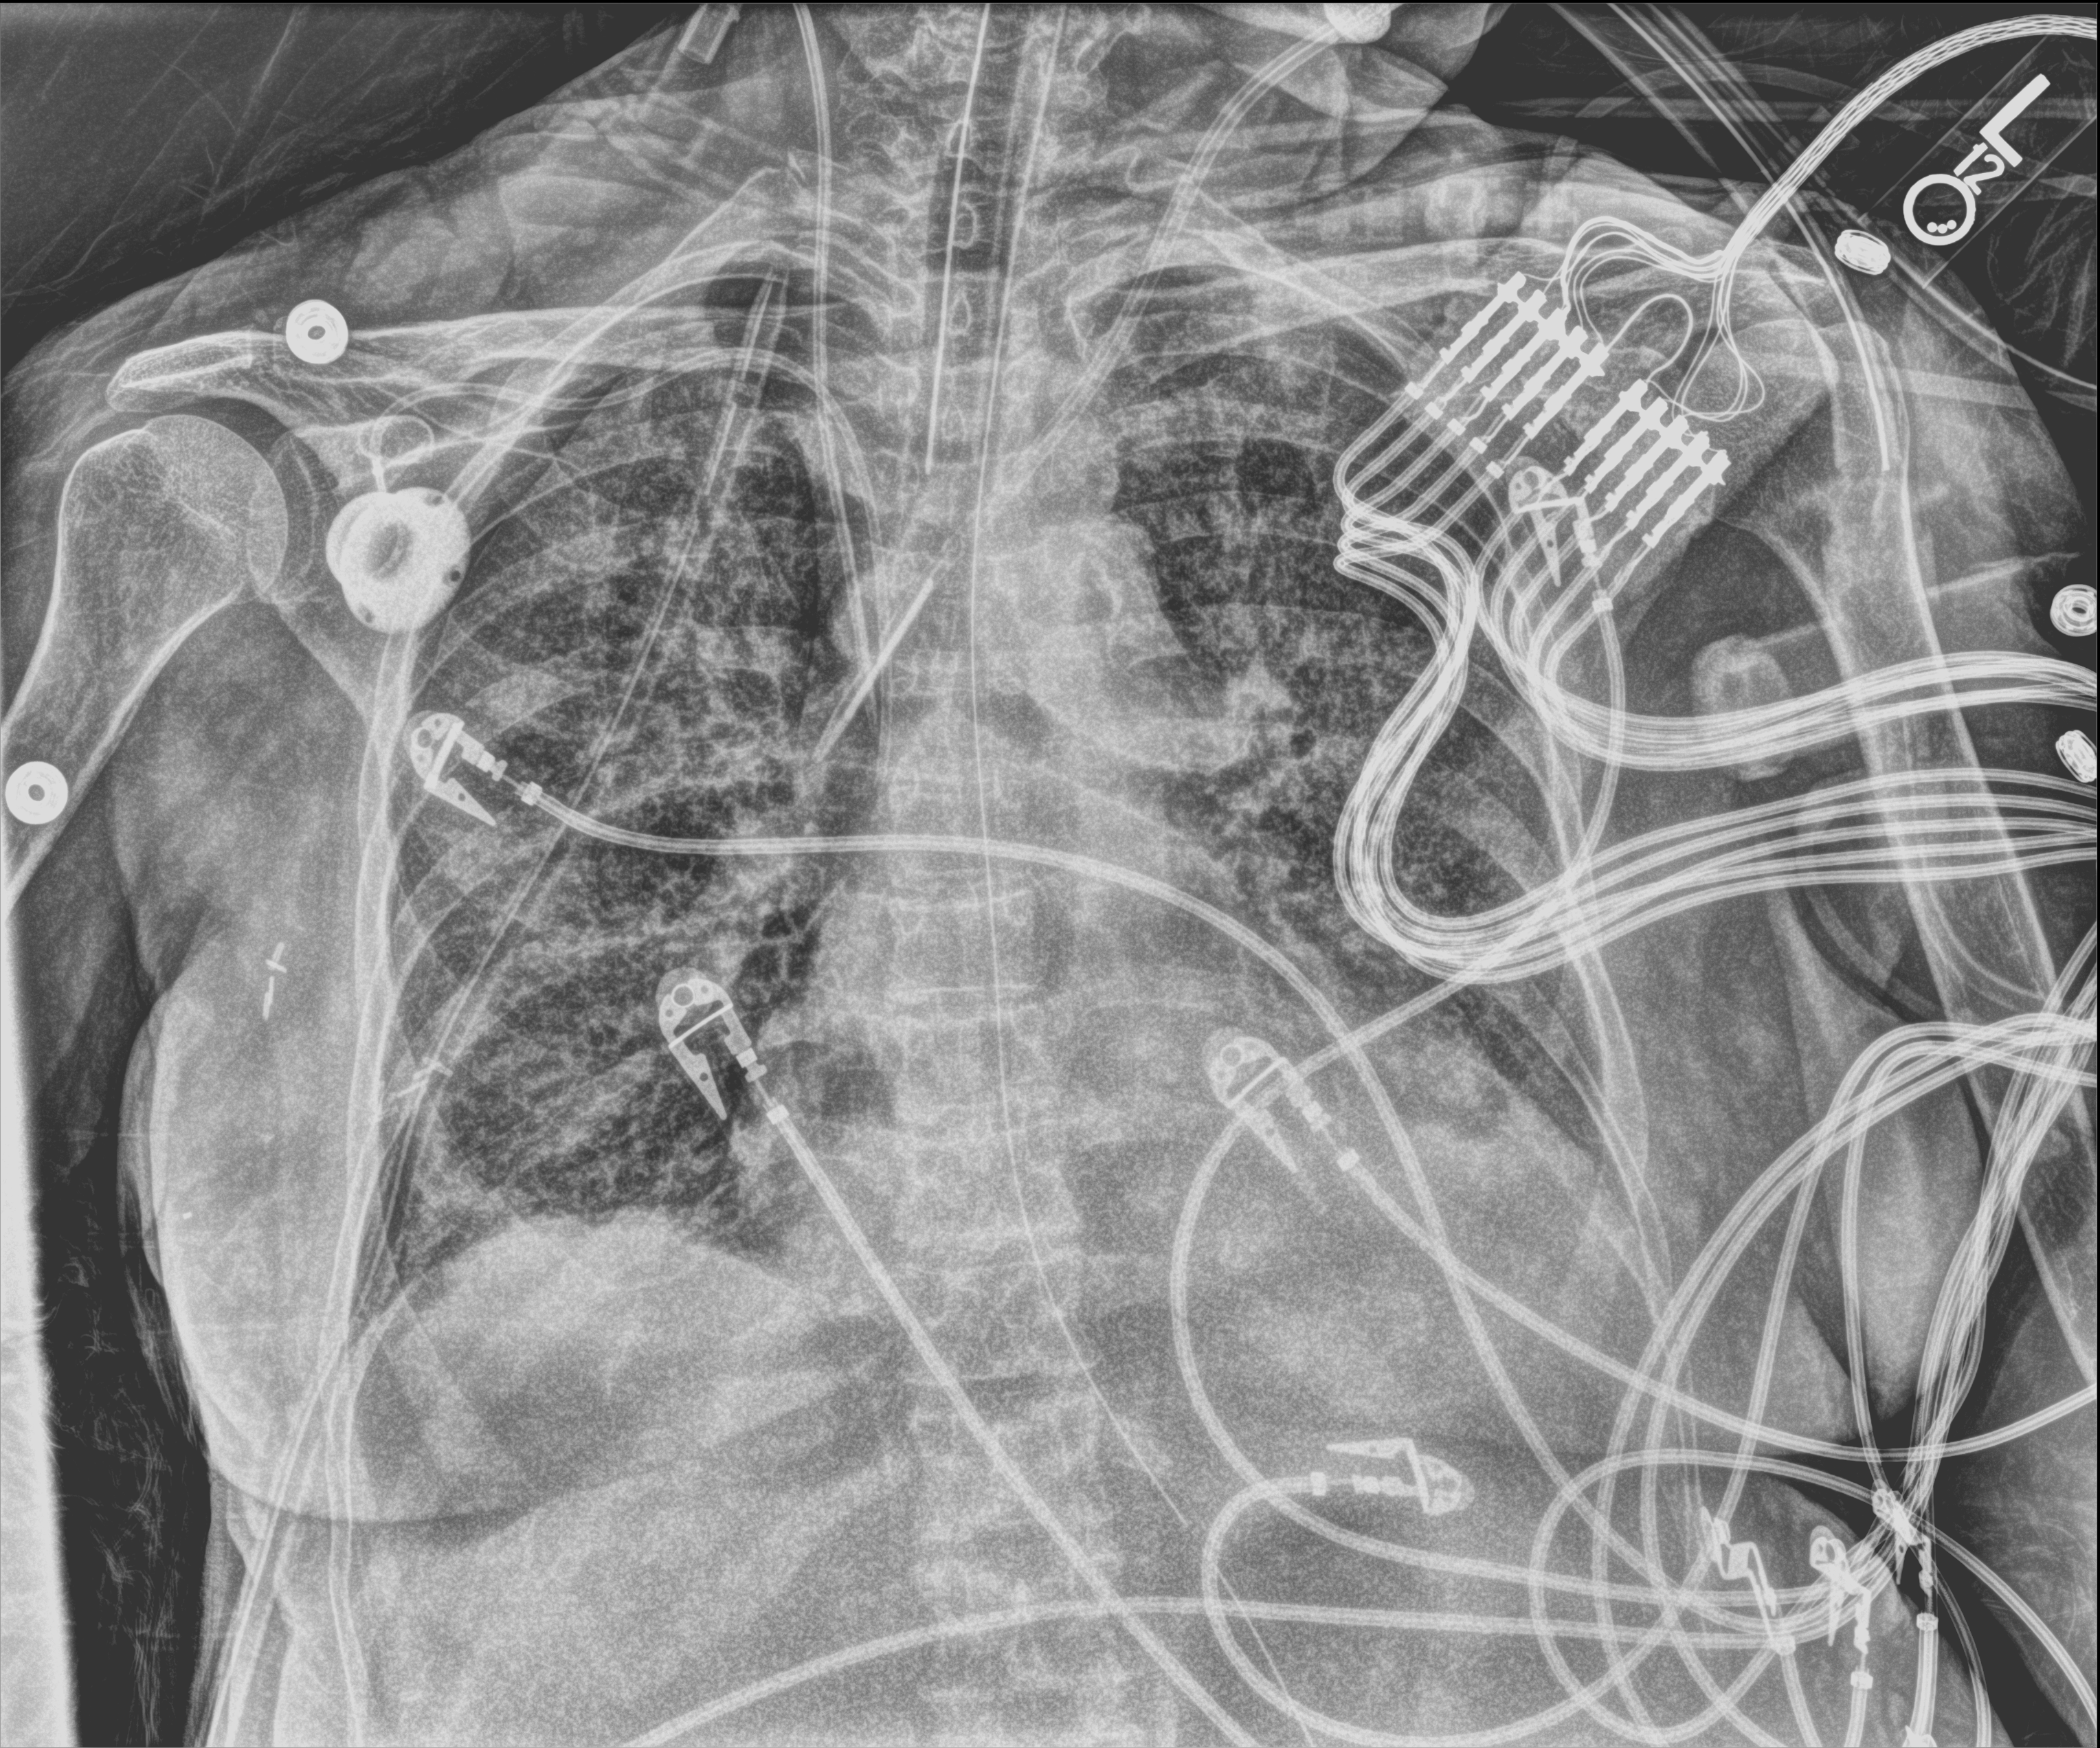
Chest X-ray (portable); anteroposterior (AP) projection. Patient hospitalised with COVID-19; female, aged 60–74 years.
Admission-level facts for this patient (not findings on this image; timing relative to this image not recorded): mechanically ventilated during this hospital stay: yes; COPD (admission record): no.